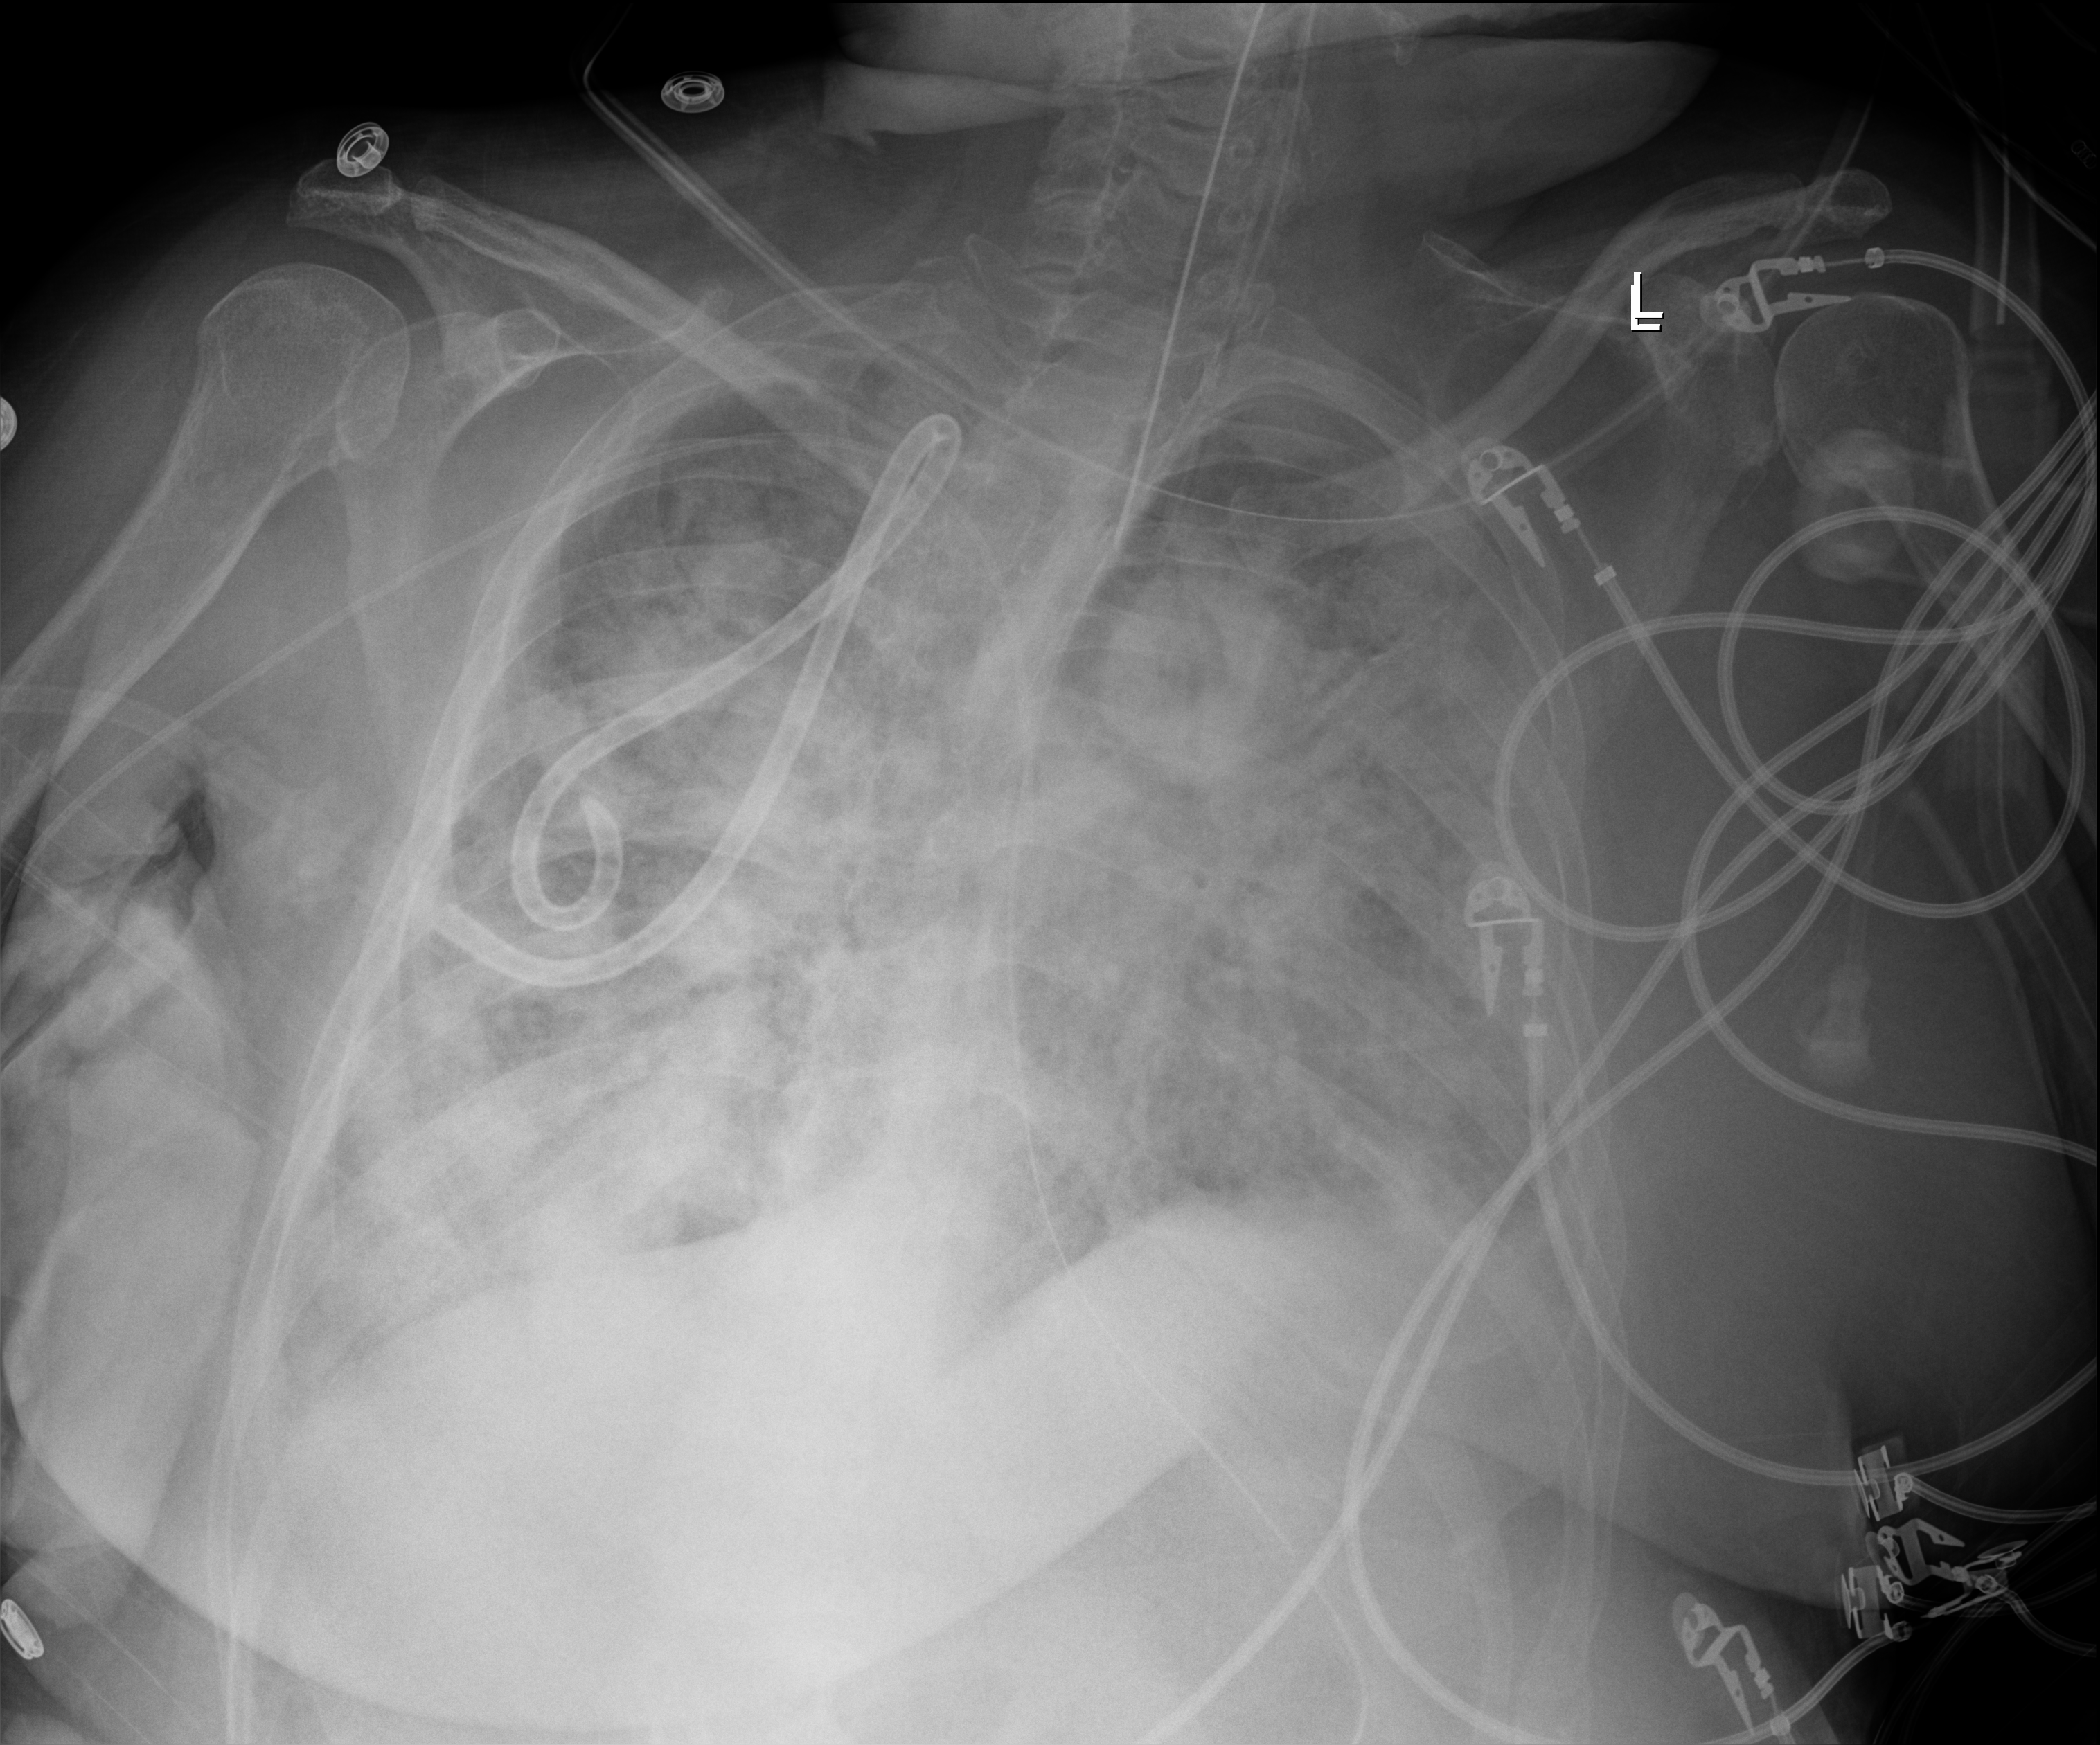
Chest X-ray (portable), anteroposterior (AP) projection. Adult patient hospitalised with COVID-19, age 18–59 years.
From the hospital-stay record, not from the radiograph (when in the stay this image was taken is not recorded):
- mechanically ventilated during this hospital stay: yes